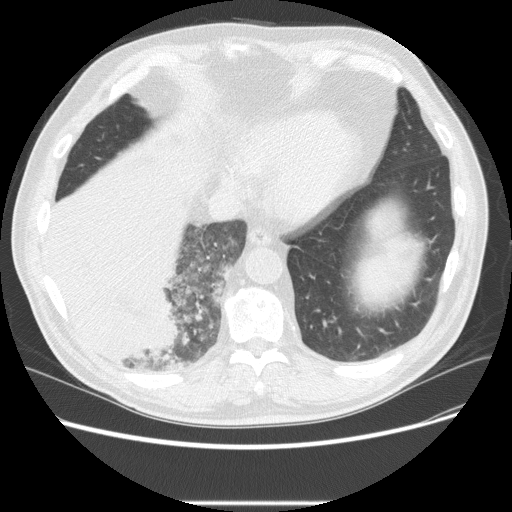
Low-dose screening chest CT, one axial slice. Slice 59 of 233 in the series (ordered by position). Reconstruction kernel STANDARD. Lung window (W 1500 / L -600 HU). 2.5 mm slice thickness. 512 × 512 image matrix, field of view 380 × 380 mm.
Annotated regions visible in this slice (expert manual segmentation):
- lesion 3 (tumor, lower lobe of right lung): bounding box [x1, y1, x2, y2] px = [47, 191, 183, 372]